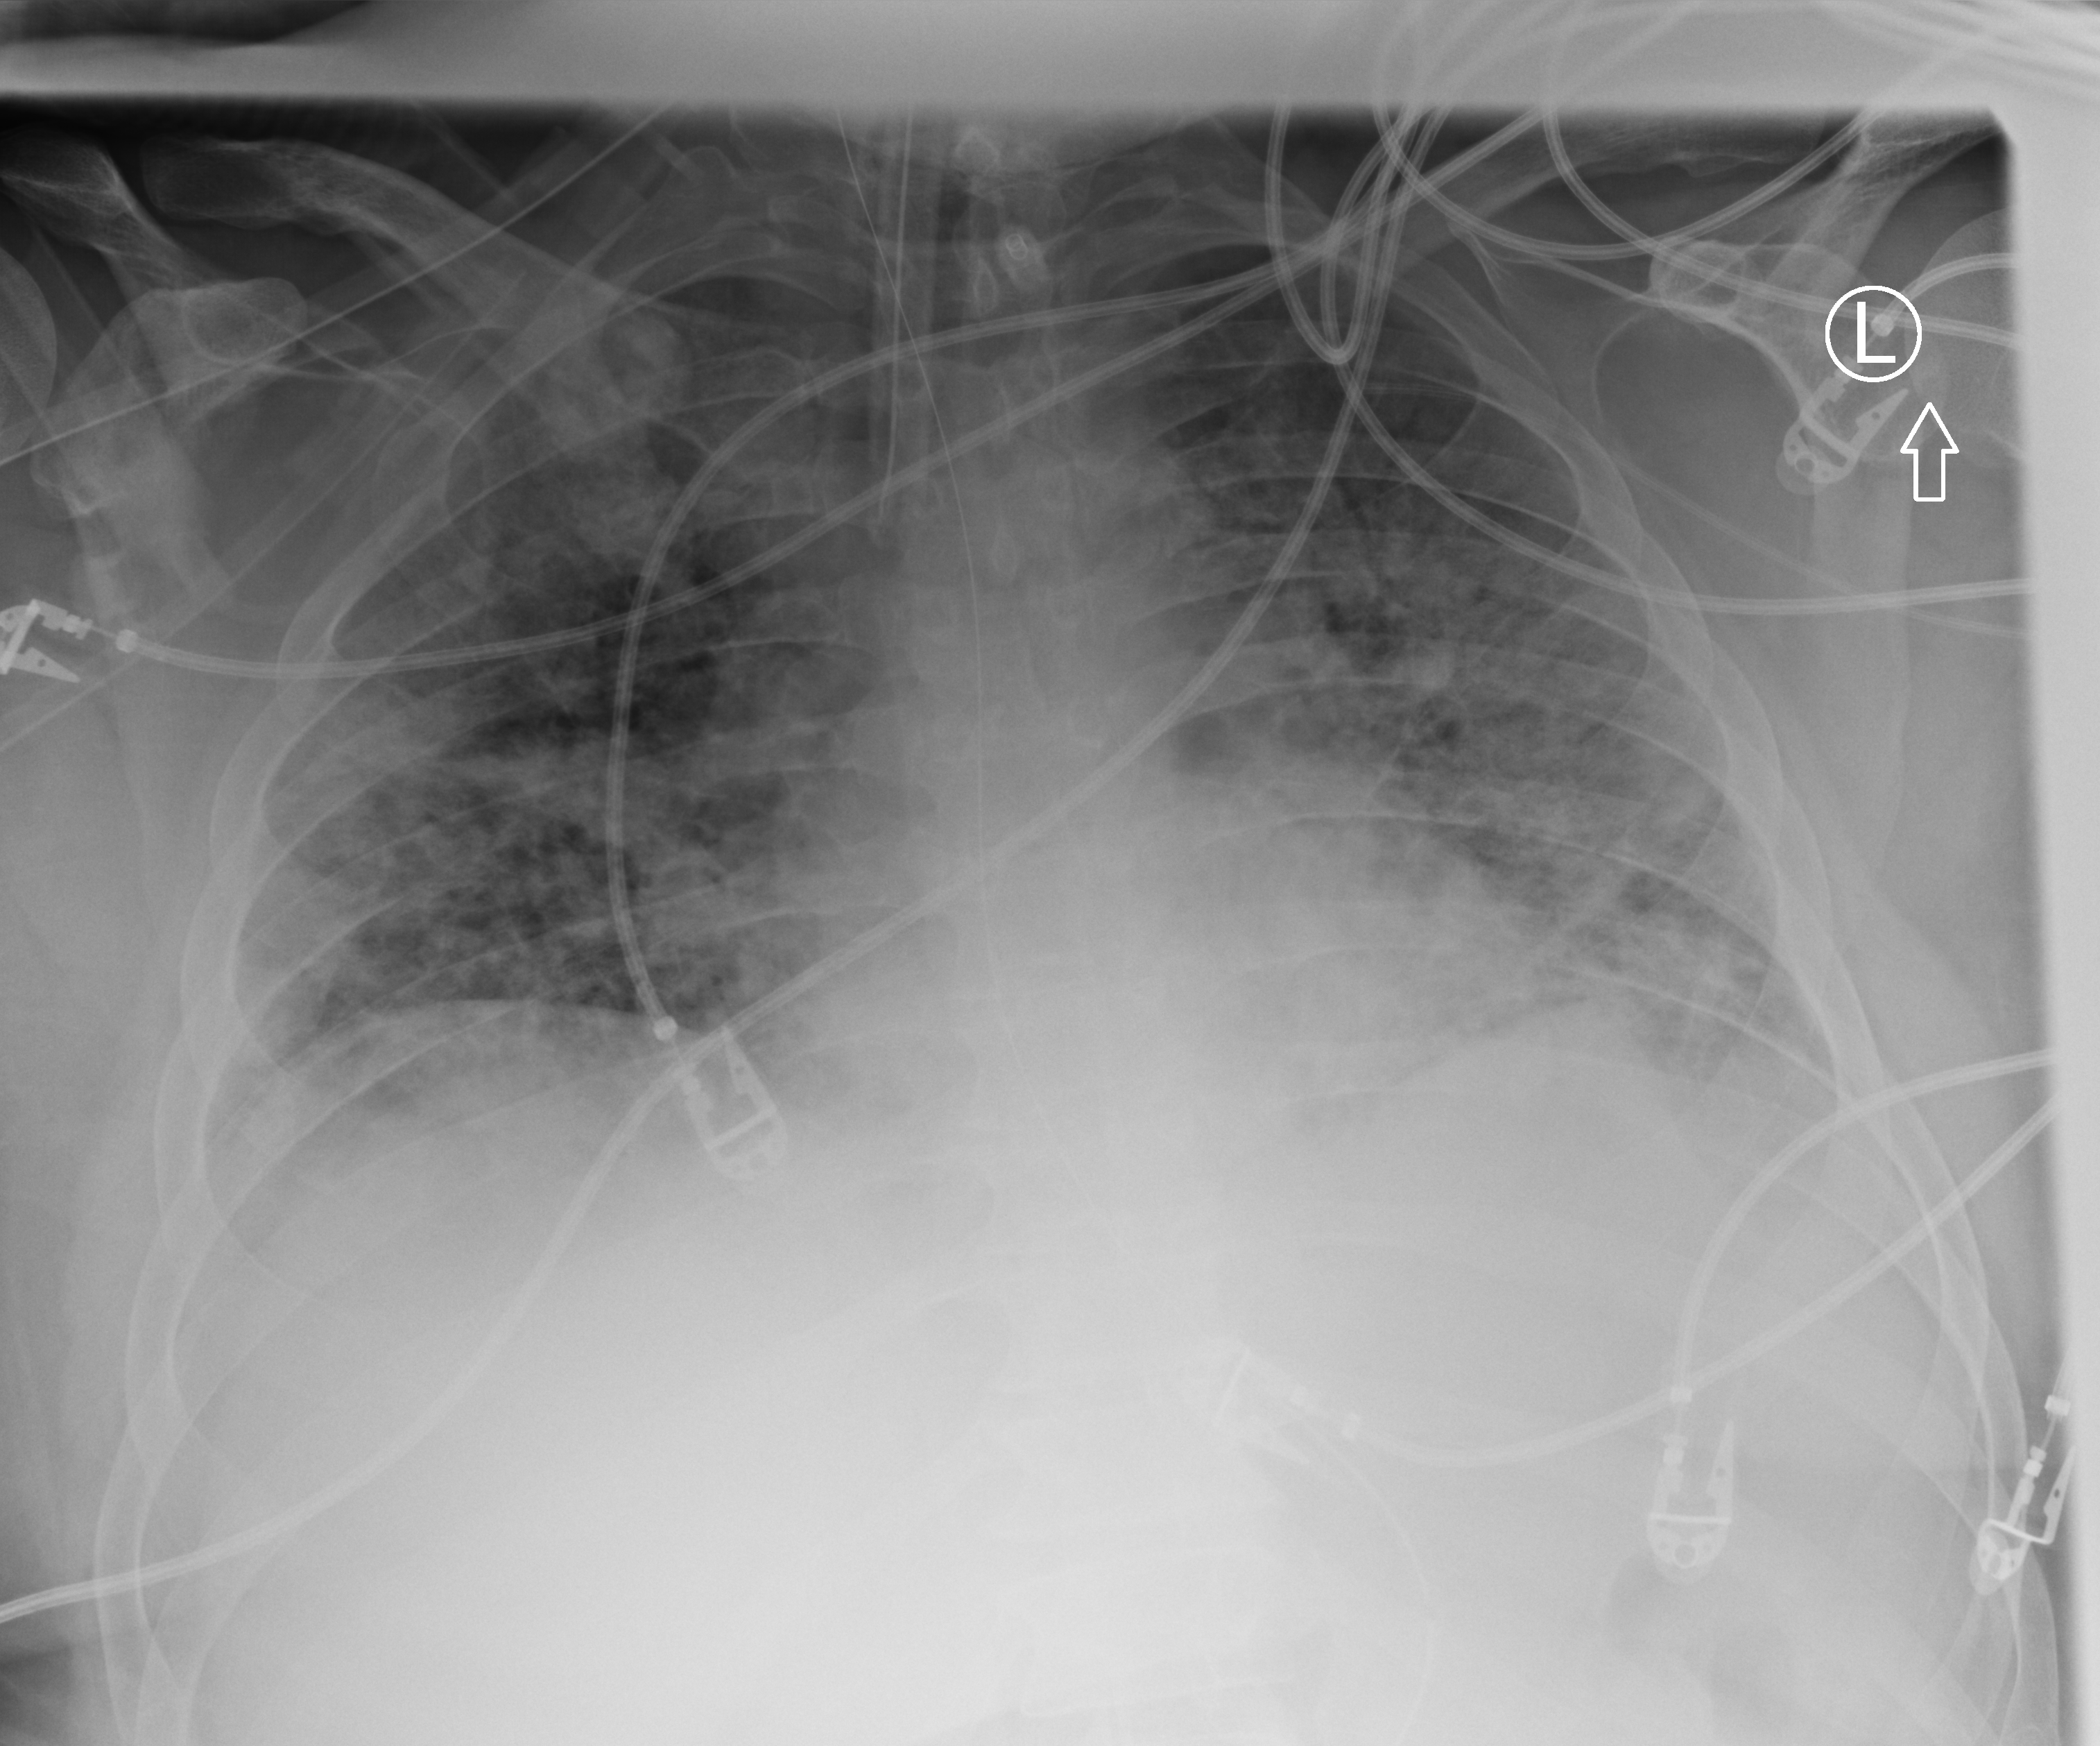
Bedside chest radiograph (computed radiography); anteroposterior (AP) projection. Adult patient hospitalised with COVID-19, age 18–59 years.
Admission-level facts for this patient (not findings on this image; timing relative to this image not recorded): length of hospital stay: 31 days; mechanically ventilated during this hospital stay: yes.